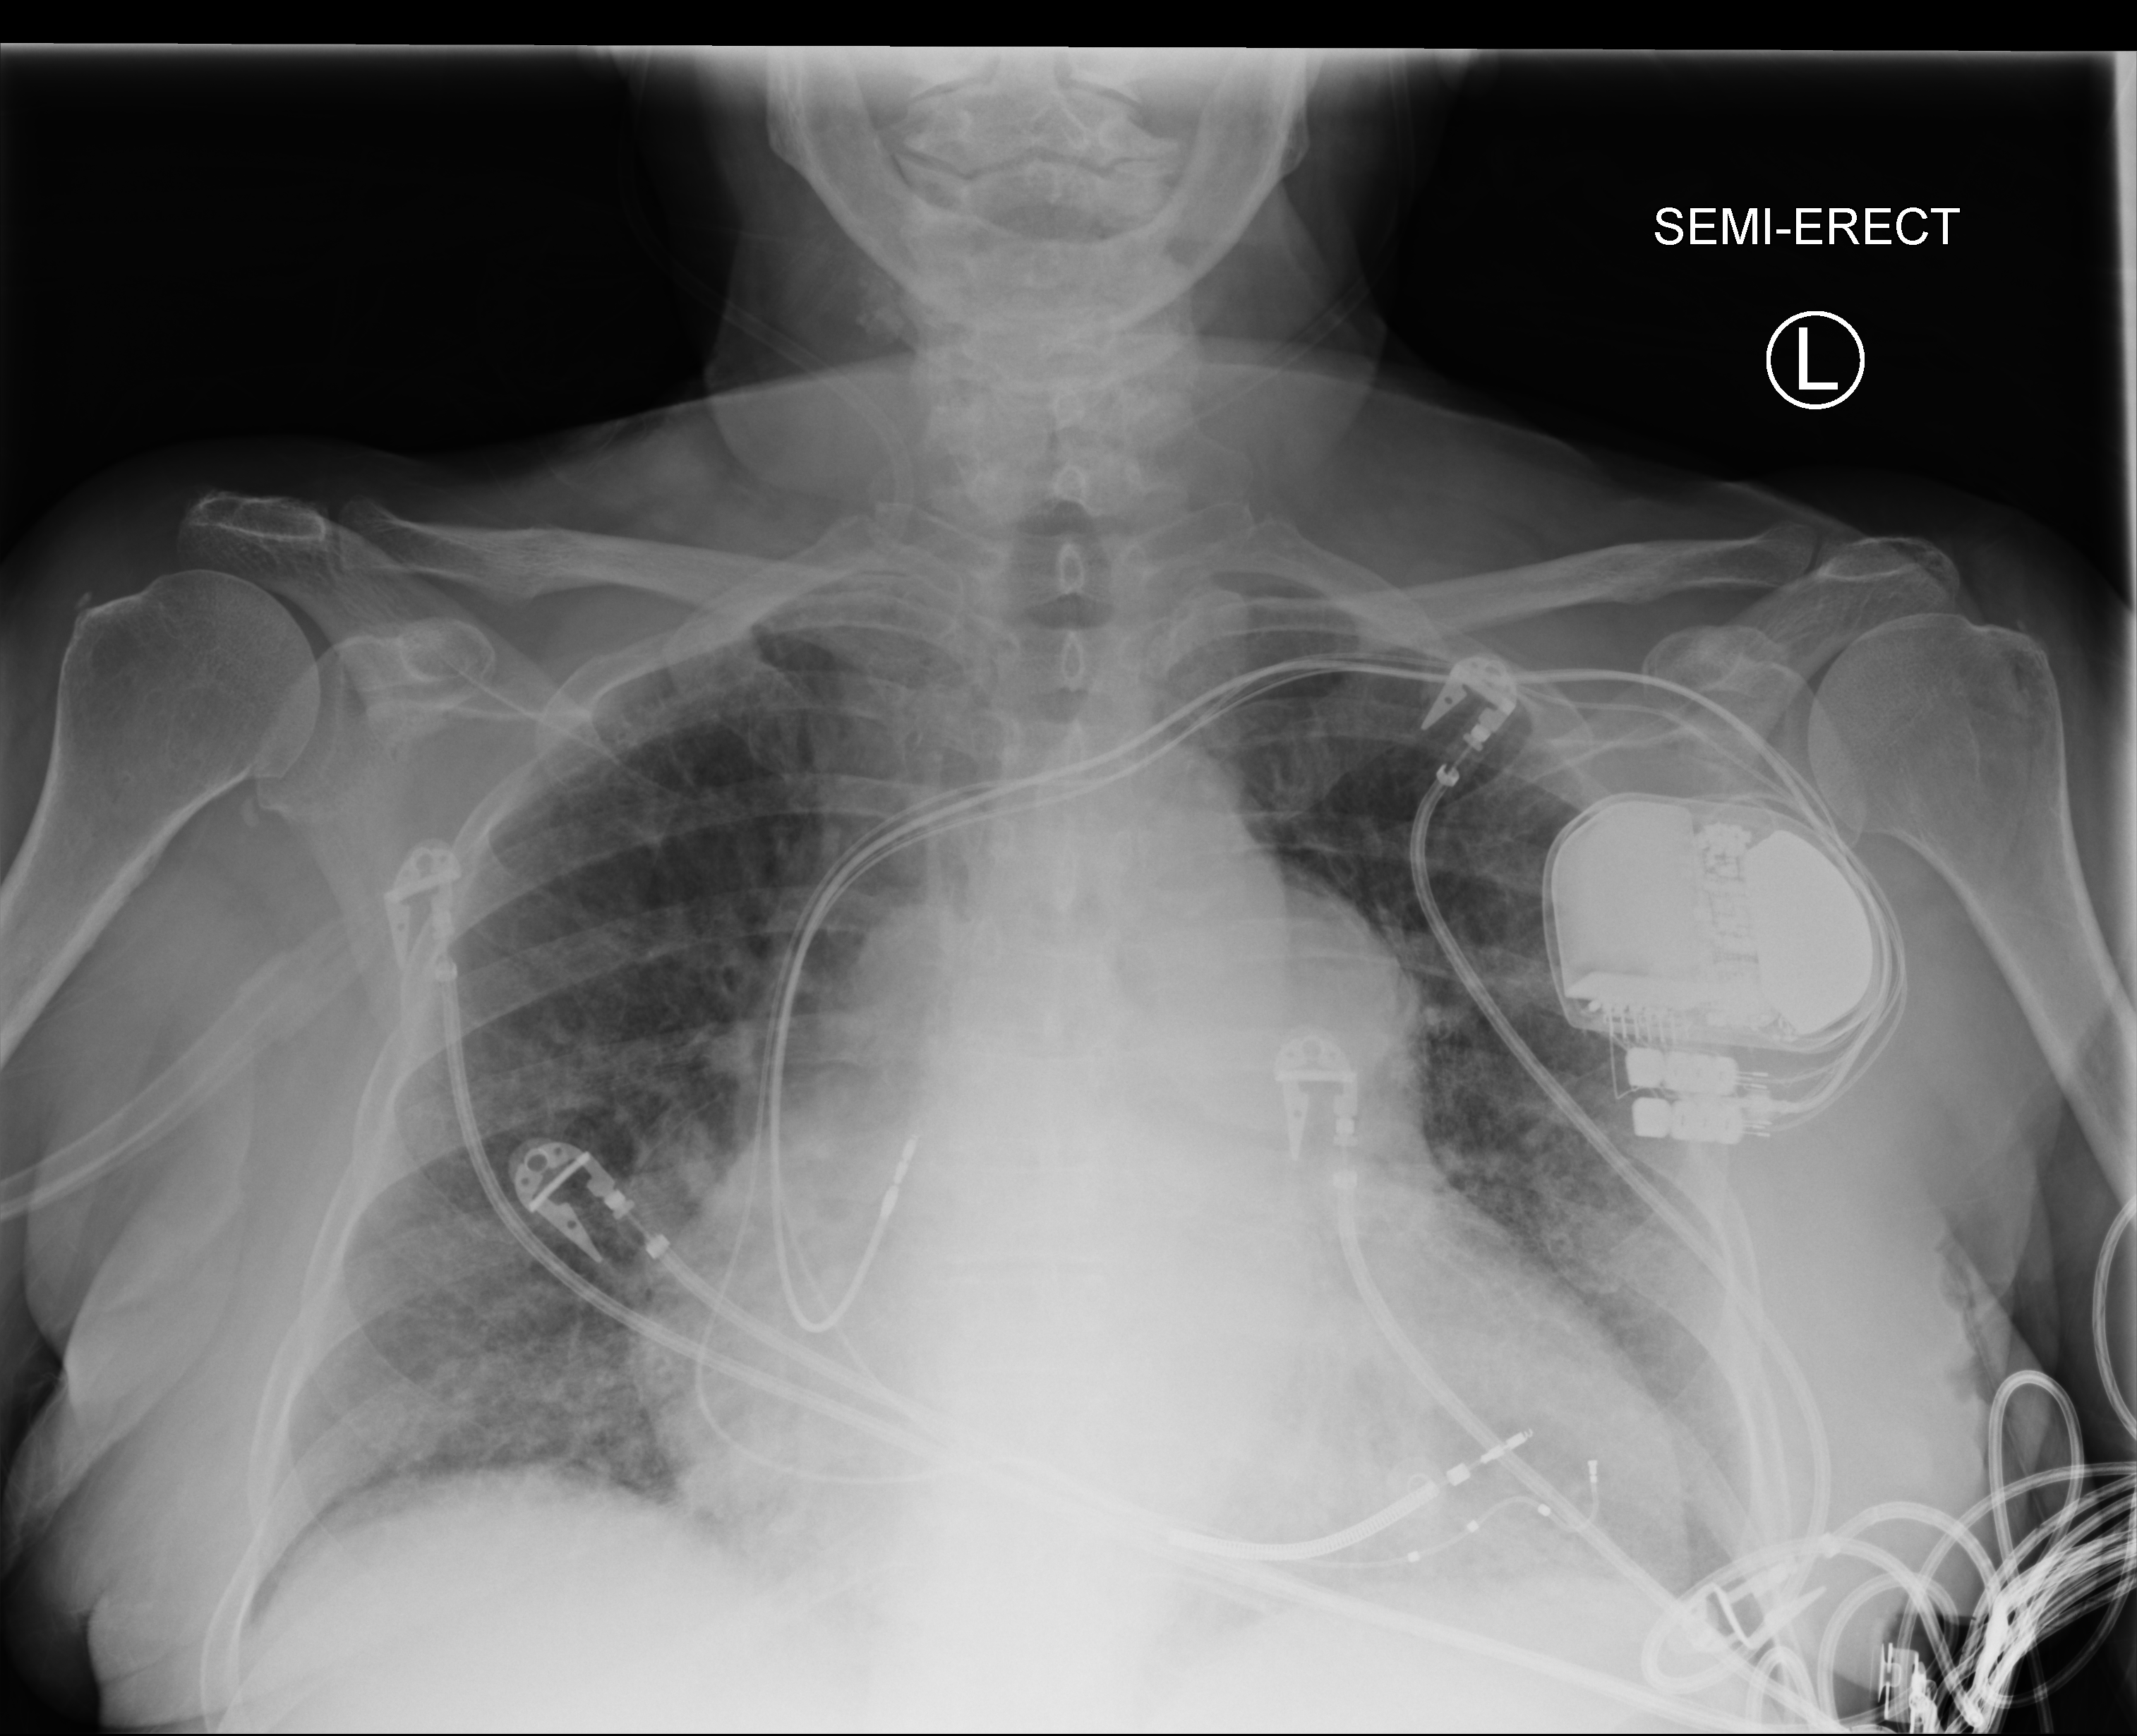
Portable chest radiograph. Patient hospitalised with COVID-19; female, aged 60–74 years.
Hospital-stay facts (about this admission, not read from this image; timing relative to this image not recorded): mechanically ventilated during this hospital stay: no.